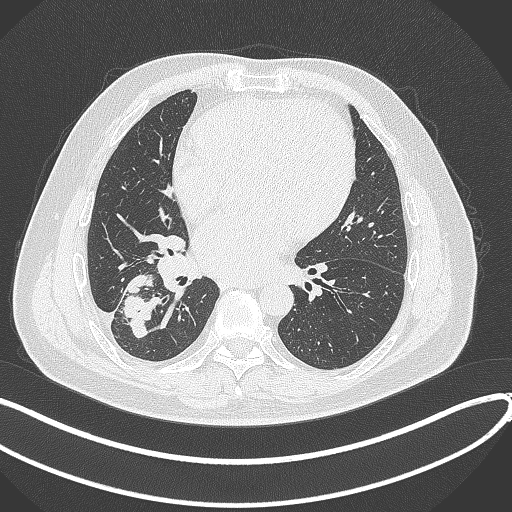
Chest CT, one axial slice. Slice 163 of 360 in the series (ordered by position). Reconstruction kernel B70f. 120 kVp. Lung window (W 1500 / L -600 HU). 1 mm slice thickness. 512 × 512 image matrix, field of view 400 × 400 mm. Patient: male, 59 years.
Structures marked on this image (bounding box drawn by a radiologist):
- lung tumour (recorded histology: adenocarcinoma): bounding box [x1, y1, x2, y2] px = [122, 274, 162, 340]